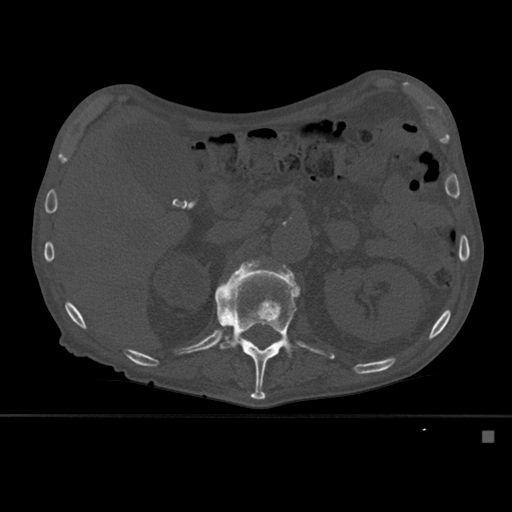
CT including the spine, one axial slice. Slice 255 of 527 in the series (ordered by position). Bone window (W 1800 / L 400 HU). 1.5 mm slice thickness. 512 × 512 image matrix, field of view 373 × 373 mm. Patient: male, 78 years. Case-level facts recorded for this patient, not image findings: primary cancer: prostate.
Structures marked on this image (semi-automatically segmented with operator editing):
- L1 vertebra: bounding box (x1, y1, x2, y2) in pixels: (215, 263, 300, 400)